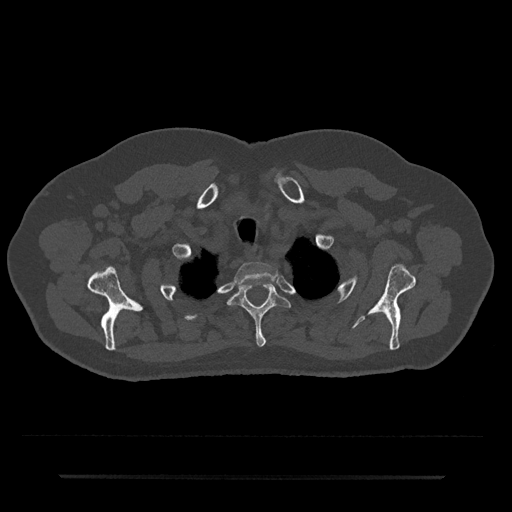
CT including the spine, one axial slice. Slice 611 of 797 in the series (ordered by position). 120 kVp. Bone window (W 1800 / L 400 HU). 512 × 512 image matrix, field of view 437 × 437 mm. Patient: male, 69 years. Case-level facts recorded for this patient, not image findings: primary cancer: prostate.
Annotated regions visible in this slice (semi-automatic segmentation, software-assisted and operator-edited):
- T1 vertebra: bounding box [x1, y1, x2, y2] px = [235, 262, 279, 285]
- T2 vertebra: [227, 283, 292, 347]